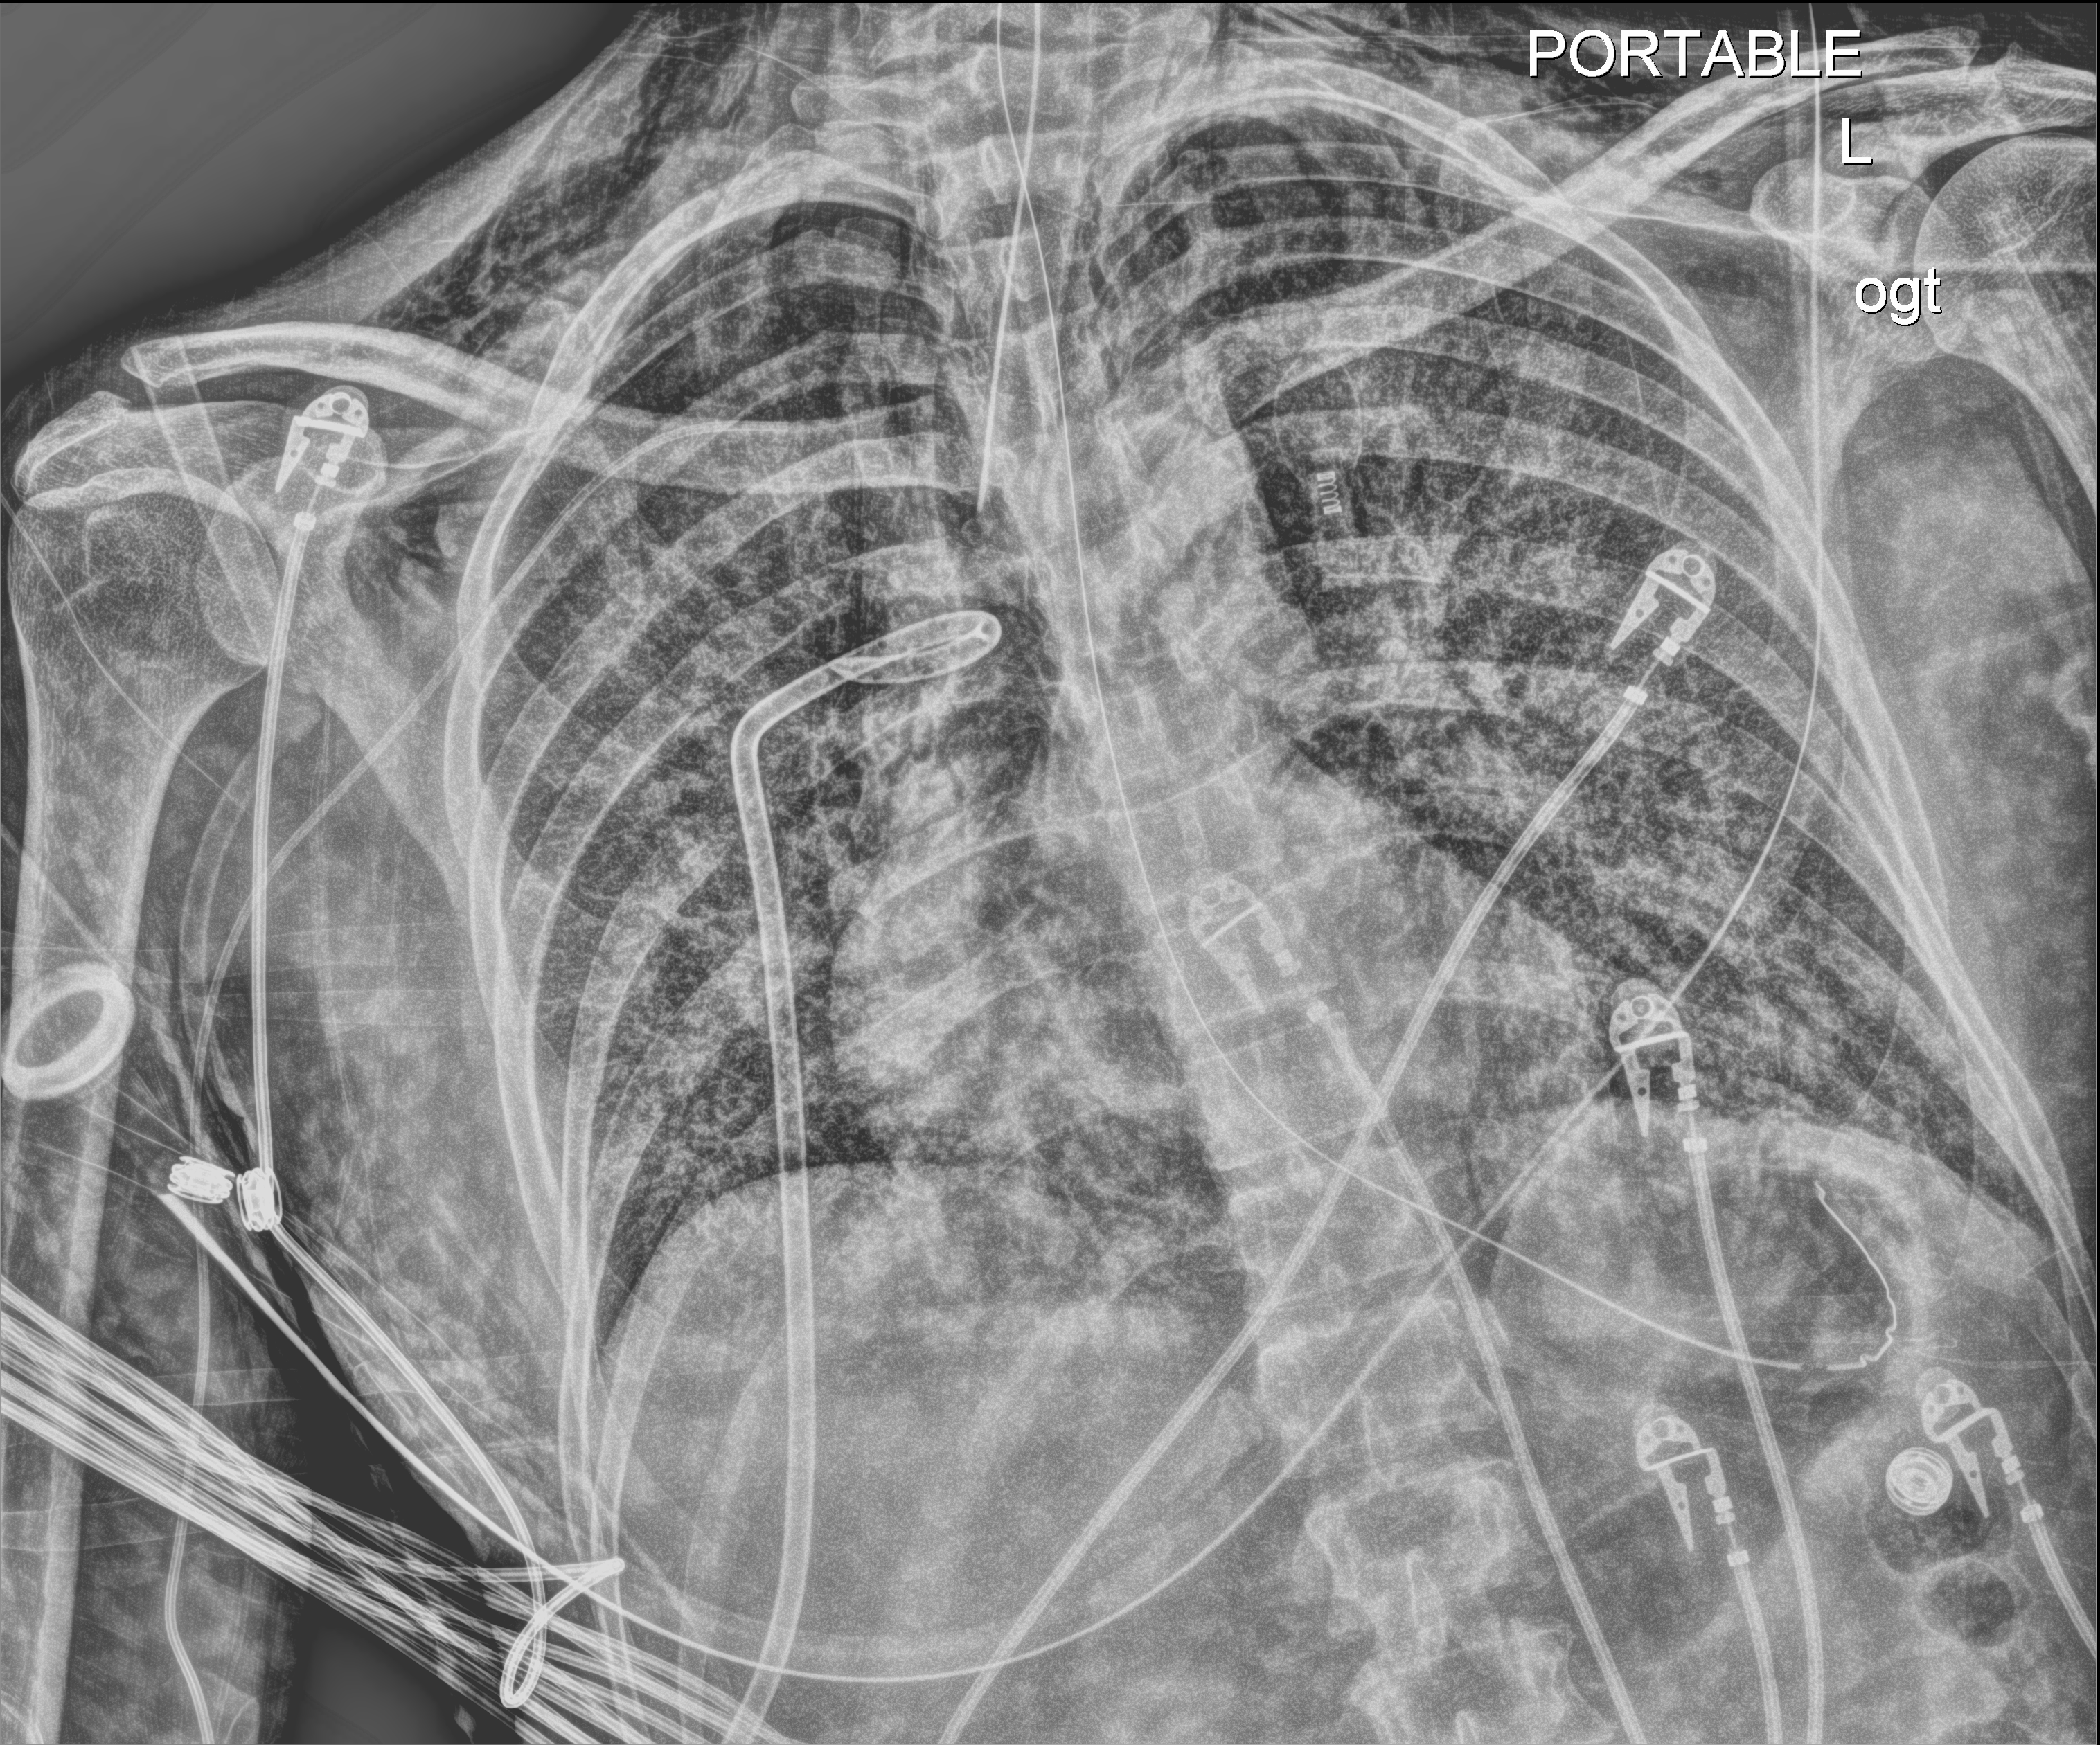
Chest X-ray, anteroposterior (AP) projection. Patient hospitalised with COVID-19, aged 18–59 years.
From the hospital-stay record, not from the radiograph (when in the stay this image was taken is not recorded): diabetes (admission record): no; smoking status (admission record): never; mechanically ventilated during this hospital stay: yes.